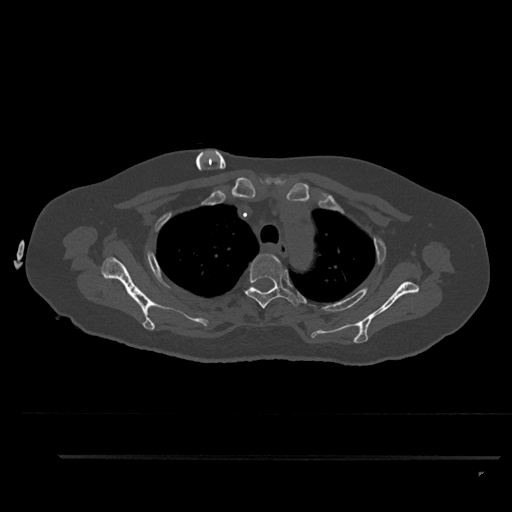
CT including the spine, one axial slice; 120 kVp; bone window (W 1800 / L 400 HU); 0.5 mm slice thickness; 512 × 512 image matrix, field of view 408 × 408 mm. Patient: female, 44 years. From the clinical record (not read from this slice): primary cancer: renal; vertebrae with lytic lesions (as recorded): L1.
Outlined on this slice (semi-automatic segmentation, software-assisted and operator-edited):
- T3 vertebra: box from (x=245, y=254) to (x=300, y=309) px